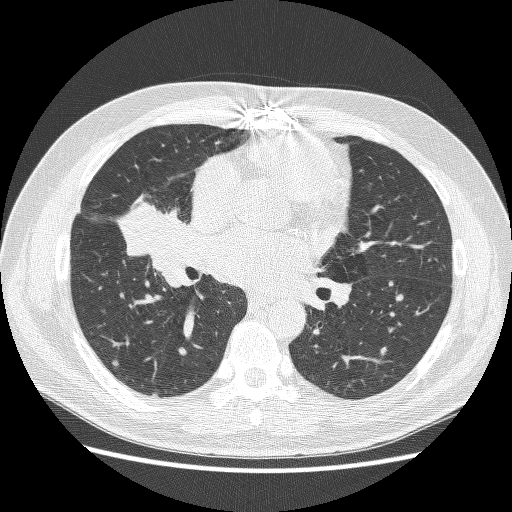
Low-dose screening chest CT, axial slice. Baseline annual screen. Lung window (W 1500 / L -600 HU). 120 kVp. 512 × 512 image matrix. Male participant, aged 59 years at enrolment.
• Expert reader's lesion annotation, bounding box (x1, y1, x2, y2) in pixels: (121, 188, 197, 262).
• No non-calcified nodule or mass ≥4 mm was recorded by the screening reader at this exam.
• Later outcome: lung cancer diagnosed 24 days after this screen — adenocarcinoma, NOS, right middle lobe, poorly differentiated (G3), stage IV (AJCC 6th edition), 54 mm at pathology.